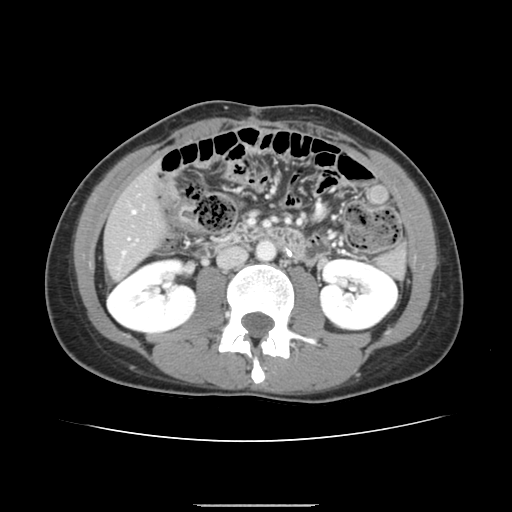
Contrast-enhanced abdominal CT, one axial slice. Slice 50 of 150 in the series (ordered by position). 120 kVp. Intravenous contrast given. Soft-tissue window (W 400 / L 40 HU). 2.5 mm slice thickness. 512 × 512 image matrix, field of view 324 × 324 mm. Female patient, age 32 years. From the clinical record (not read from this slice): diagnosis: colorectal cancer liver metastases, imaged before liver resection; multiple liver metastases: yes; largest metastasis: 0.7 cm; disease in both lobes: no.
Outlined on this slice (manually delineated by an expert):
- hepatic veins: bounding box <133,210,136,213> (left, top, right, bottom; pixels)
- liver: <105,168,163,279>
- planned liver remnant (the part of the liver to remain after resection): <105,168,163,278>